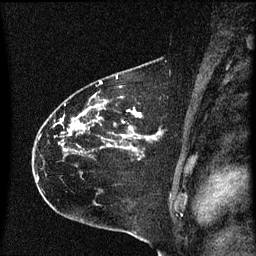
Breast MRI (dynamic contrast-enhanced), one sagittal slice; slice 43 of 60 in the series (ordered by position); dynamic contrast-enhanced series, image 2 of 3 at this slice position (ordered by acquisition); 1.5 T; TE 4.2 ms, TR 8.4 ms; 2 mm slice thickness; 256 × 256 image matrix, field of view 200 × 200 mm. Patient: female, 35 years. From the clinical record (not read from this slice): setting: breast cancer imaged before/during neoadjuvant chemotherapy; receptor status: HER2-positive.
Outlined on this slice (semi-automatic segmentation, software-assisted and operator-edited):
- analysis volume of interest (the breast-tissue region the enhancement analysis was run in; not a lesion): box from (x=35, y=68) to (x=171, y=173) px
- tumour enhancement mask (voxels above the 70 % enhancement threshold inside the analysis volume of interest): (x=38, y=76)–(x=159, y=149)